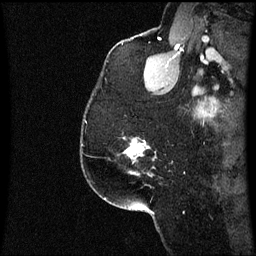
Breast MRI (dynamic contrast-enhanced), one sagittal slice. Slice 48 of 60 in the series (ordered by position). Dynamic contrast-enhanced series, image 2 of 3 at this slice position (ordered by acquisition). 1.5 T. TE 4.2 ms, TR 8.9 ms. 2 mm slice thickness. 256 × 256 image matrix, field of view 200 × 200 mm. Patient: female, 58 years. Case-level facts recorded for this patient, not image findings: setting: breast cancer imaged before/during neoadjuvant chemotherapy; receptor status: triple-negative.
Structures marked on this image (semi-automatic segmentation, software-assisted and operator-edited):
- analysis volume of interest (the breast-tissue region the enhancement analysis was run in; not a lesion): bounding box [x1, y1, x2, y2] px = [124, 138, 157, 177]
- tumour enhancement mask (voxels above the 70 % enhancement threshold inside the analysis volume of interest): [126, 140, 145, 175]